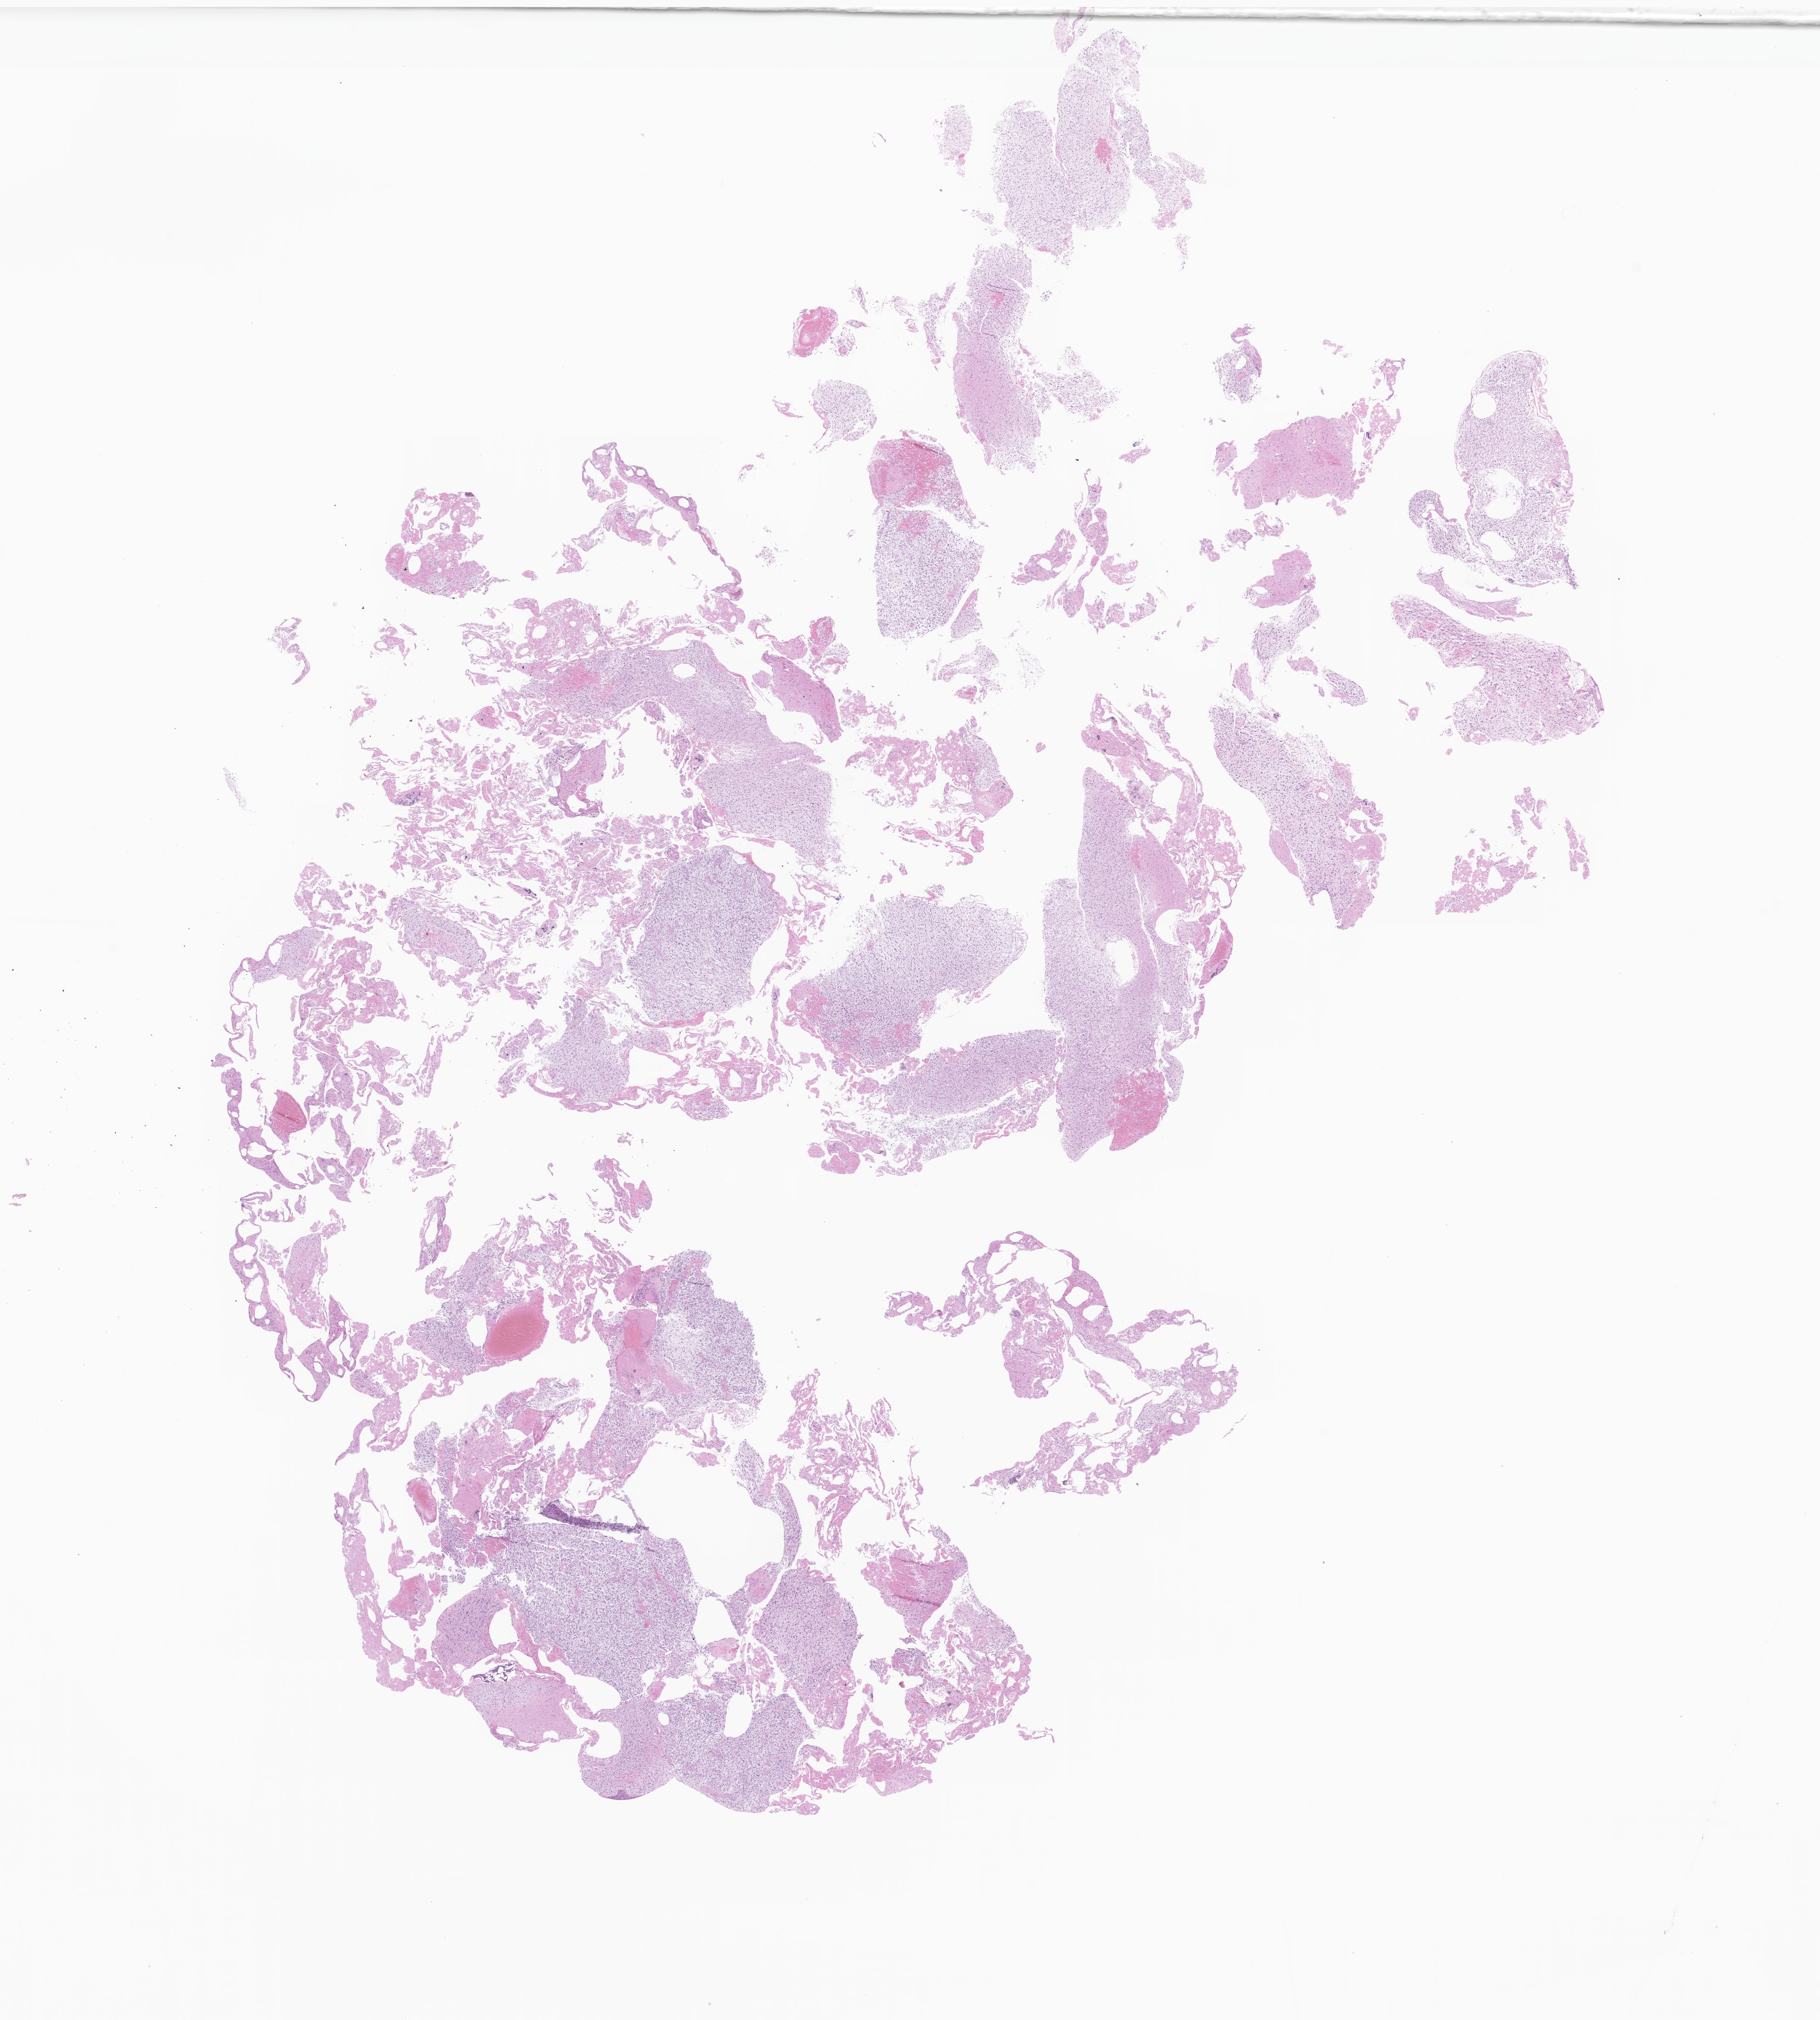
Whole-slide image, haematoxylin and eosin stain of tumor tissue from the brain stem — low-resolution overview of the scanned area, about 15.9 x 17.6 mm; formalin-fixed, paraffin-embedded (FFPE) tissue. Female patient, age 50 months (4 years 2 months).
Recorded diagnosis: Glioma, malignant.